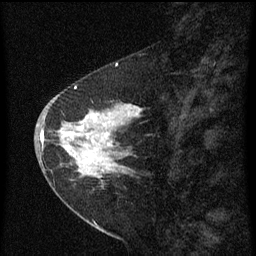
Breast MRI (dynamic contrast-enhanced), one sagittal slice. Slice 24 of 60 in the series (ordered by position). Dynamic contrast-enhanced series, image 2 of 3 at this slice position (ordered by acquisition). 1.5 T. TE 4.2 ms, TR 8 ms. 256 × 256 image matrix, field of view 180 × 180 mm. Patient: female, 47 years.
Structures marked on this image (semi-automatically segmented with operator editing):
- analysis volume of interest (the breast-tissue region the enhancement analysis was run in; not a lesion): bounding box [x1, y1, x2, y2] px = [44, 84, 151, 199]
- tumour enhancement mask (voxels above the 70 % enhancement threshold inside the analysis volume of interest): [44, 86, 143, 177]